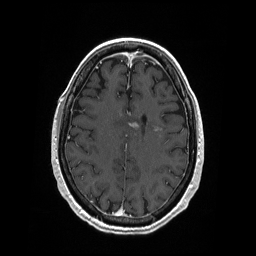
Brain MRI from a brain-tumour surgery series, one axial slice. Position 74 of 208 along the scan axis. T1-weighted post-contrast. 256 × 256 image matrix, field of view 256 × 256 mm. From the clinical record (not read from this slice): histopathology: Primary diffuse large B-cell lymphoma; tumour location: Left Corpus Callosum (Frontal).
Annotated regions visible in this slice (expert manual segmentation):
- tumour: bounding box (x1, y1, x2, y2) in pixels: (129, 121, 164, 132)